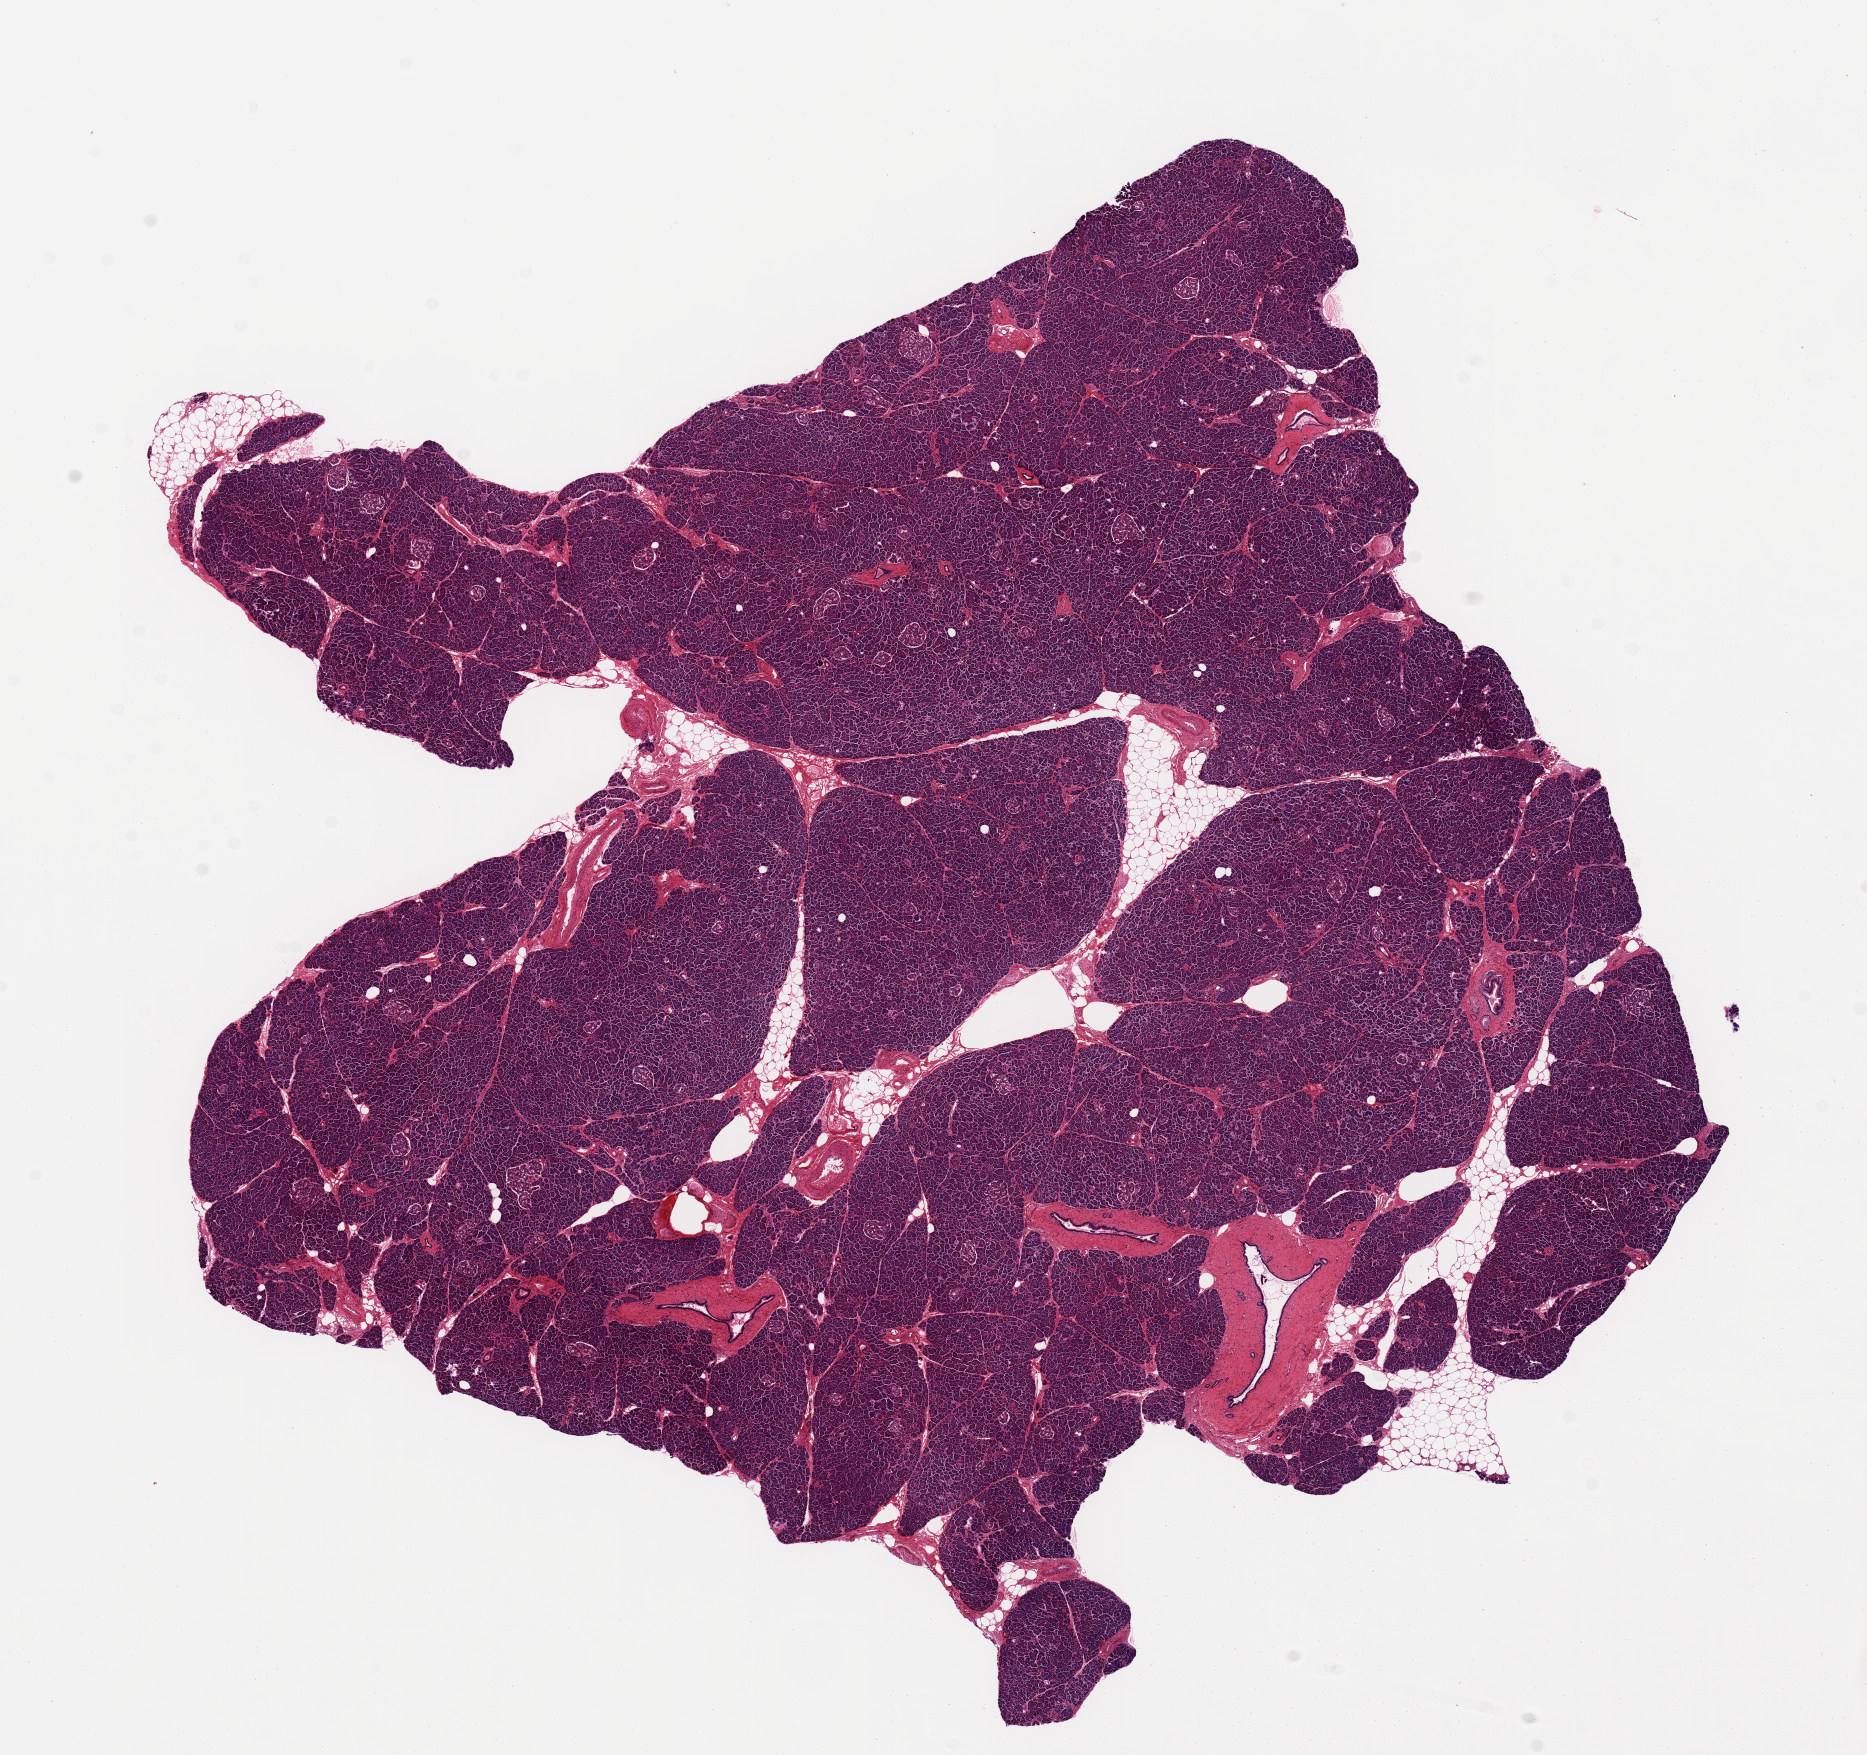
Hematoxylin and eosin (H&E) whole-slide image — whole scanned area (about 14.8 x 13.9 mm, slide scanned at 20x) shown as a low-resolution overview, PAXgene-fixed, paraffin-embedded tissue, target tissue: pancreas, donor tissue sample. Donor: male.
Review note (as recorded): 11.2x8.3mm. Well preserved, less than 5% fat.